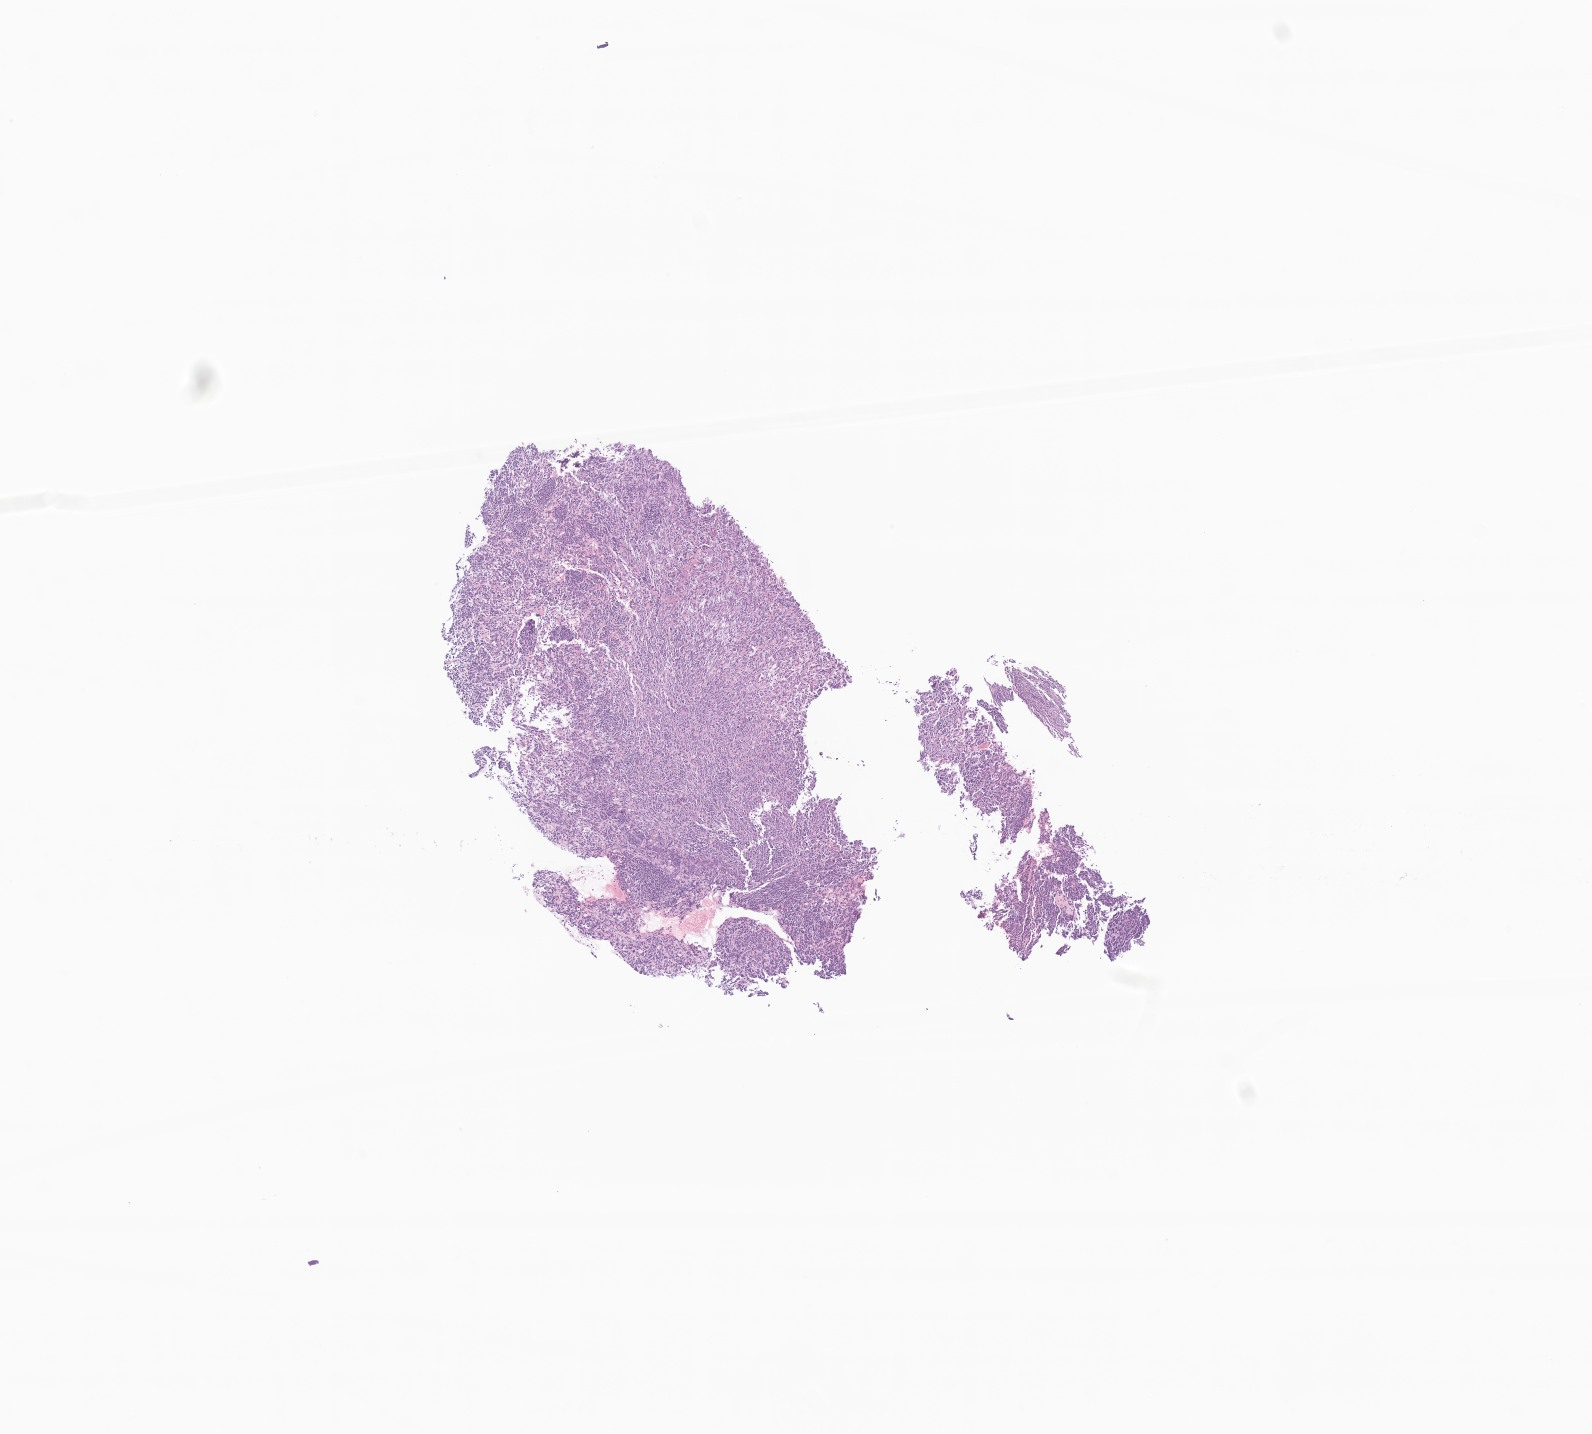
Digitized H&E-stained section of tumor tissue from the brain, whole scanned area (about 6.7 x 6.0 mm) shown as a low-resolution overview. Formalin-fixed paraffin-embedded section. Female patient, age 182 months (15 years 2 months).
Diagnosis (ICD-O-3 morphology term): Medulloblastoma, NOS.